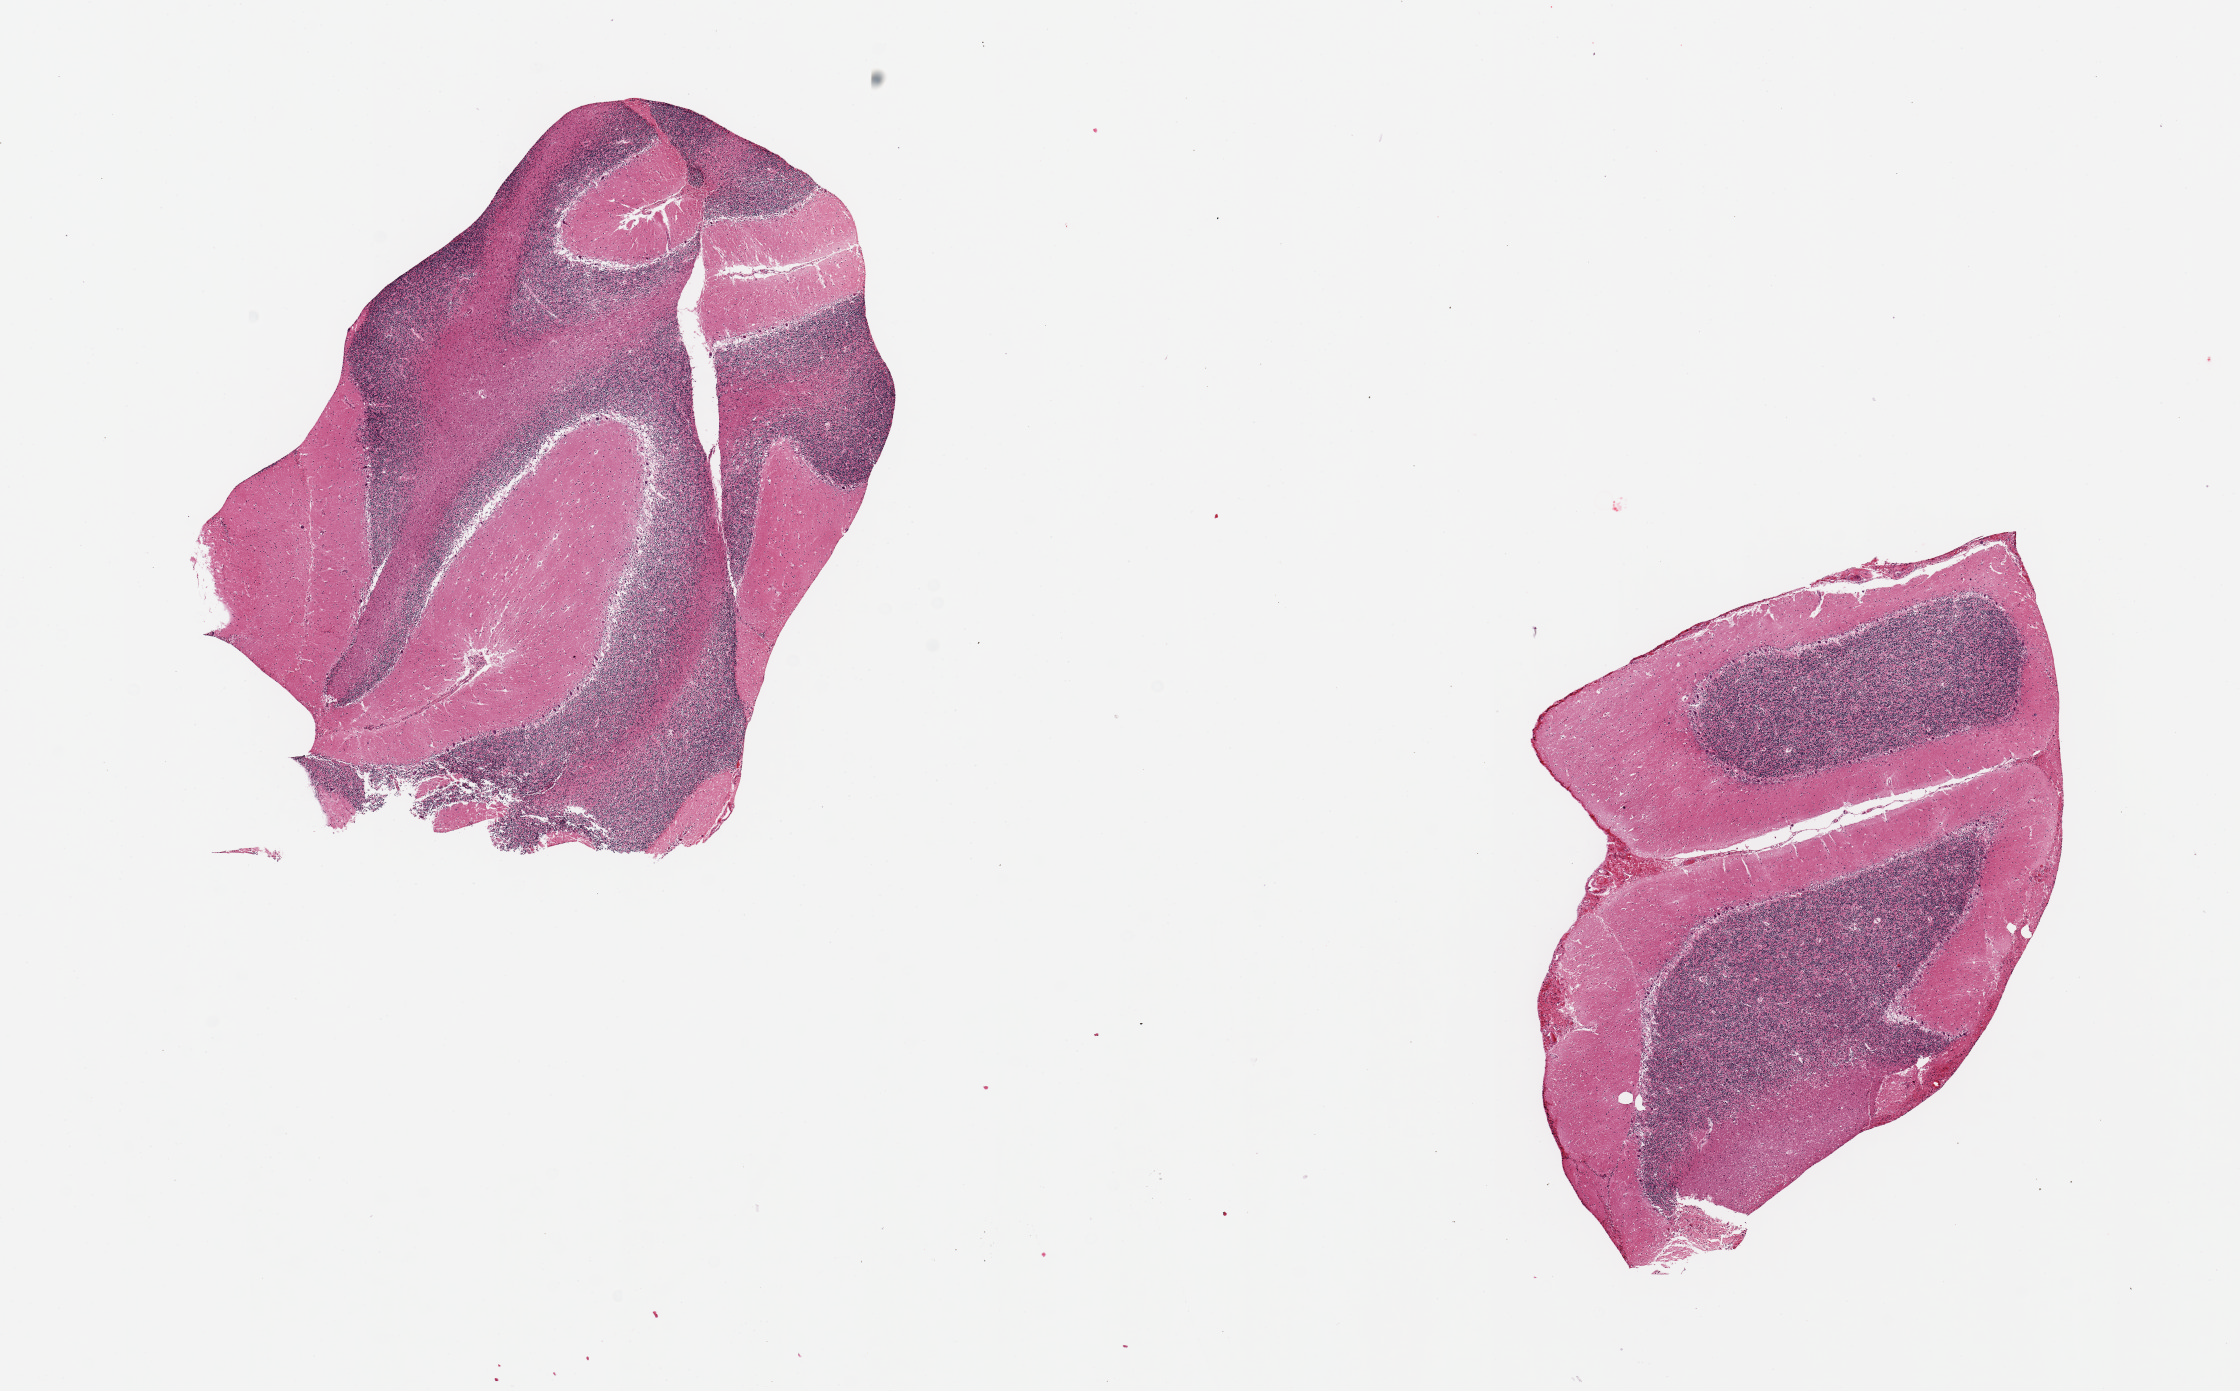
Whole-slide image, H&E stain, brightfield — shown as a low-resolution overview of the whole scanned area (about 17.7 x 11.0 mm, slide scanned at 20x). PAXgene-fixed paraffin-embedded (PFPE) section. Sampled site (target tissue): cerebellum. Tissue donor sample. Donor: male.
• pathologist's review note for this sample: 2 pieces, 6x5 & 5x4mm; good Purkinje cells